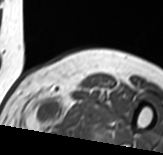
MRI of an extremity soft-tissue mass, one axial slice. Position 52 of 65 along the scan axis. MR volume resampled by the dataset authors to the PET/CT grid (not the native acquisition matrix). 3.27 mm slice thickness. 163 × 155 image matrix, field of view 159 × 151 mm. Female patient. From the clinical record (not read from this slice): histological type: pleomorphic leiomyosarcoma; grade: high; site of the primary tumour: left thigh.
Outlined on this slice (expert contour drawn on MRI and transferred to this co-registered scan by the dataset authors):
- gross tumour volume including surrounding oedema: bounding box [x1, y1, x2, y2] px = [35, 97, 86, 125]